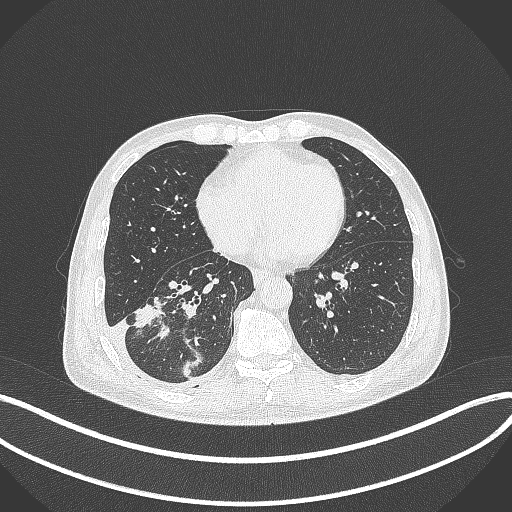
Chest CT, one axial slice. Slice 144 of 388 in the series (ordered by position). Reconstruction kernel B70f. Lung window (W 1500 / L -600 HU). 1 mm slice thickness. 512 × 512 image matrix, field of view 400 × 400 mm. Male patient, age 64 years. Case-level facts recorded for this patient, not image findings: clinical TNM (as recorded): T3 N0 M0; histopathological grade: G2-3.
Outlined on this slice (rectangle marked by the reading radiologist):
- lung tumour (recorded histology: adenocarcinoma): box from (x=129, y=299) to (x=167, y=336) px